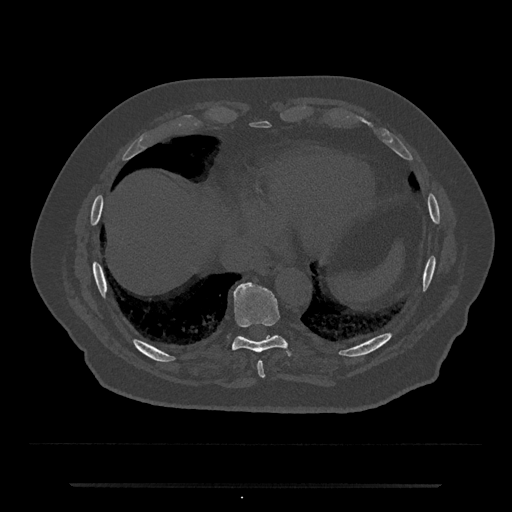
CT including the spine, one axial slice. Slice 754 of 797 in the series (ordered by position). Reconstruction kernel Br40s/3. Bone window (W 1800 / L 400 HU). 512 × 512 image matrix. Male patient, age 80 years. From the clinical record (not read from this slice): primary cancer: prostate; vertebrae with lytic lesions (as recorded): L1, T11.
Structures marked on this image (semi-automatically segmented with operator editing):
- T8 vertebra: bounding box (x1, y1, x2, y2) in pixels: (257, 361, 265, 378)
- T9 vertebra: (232, 282, 286, 353)